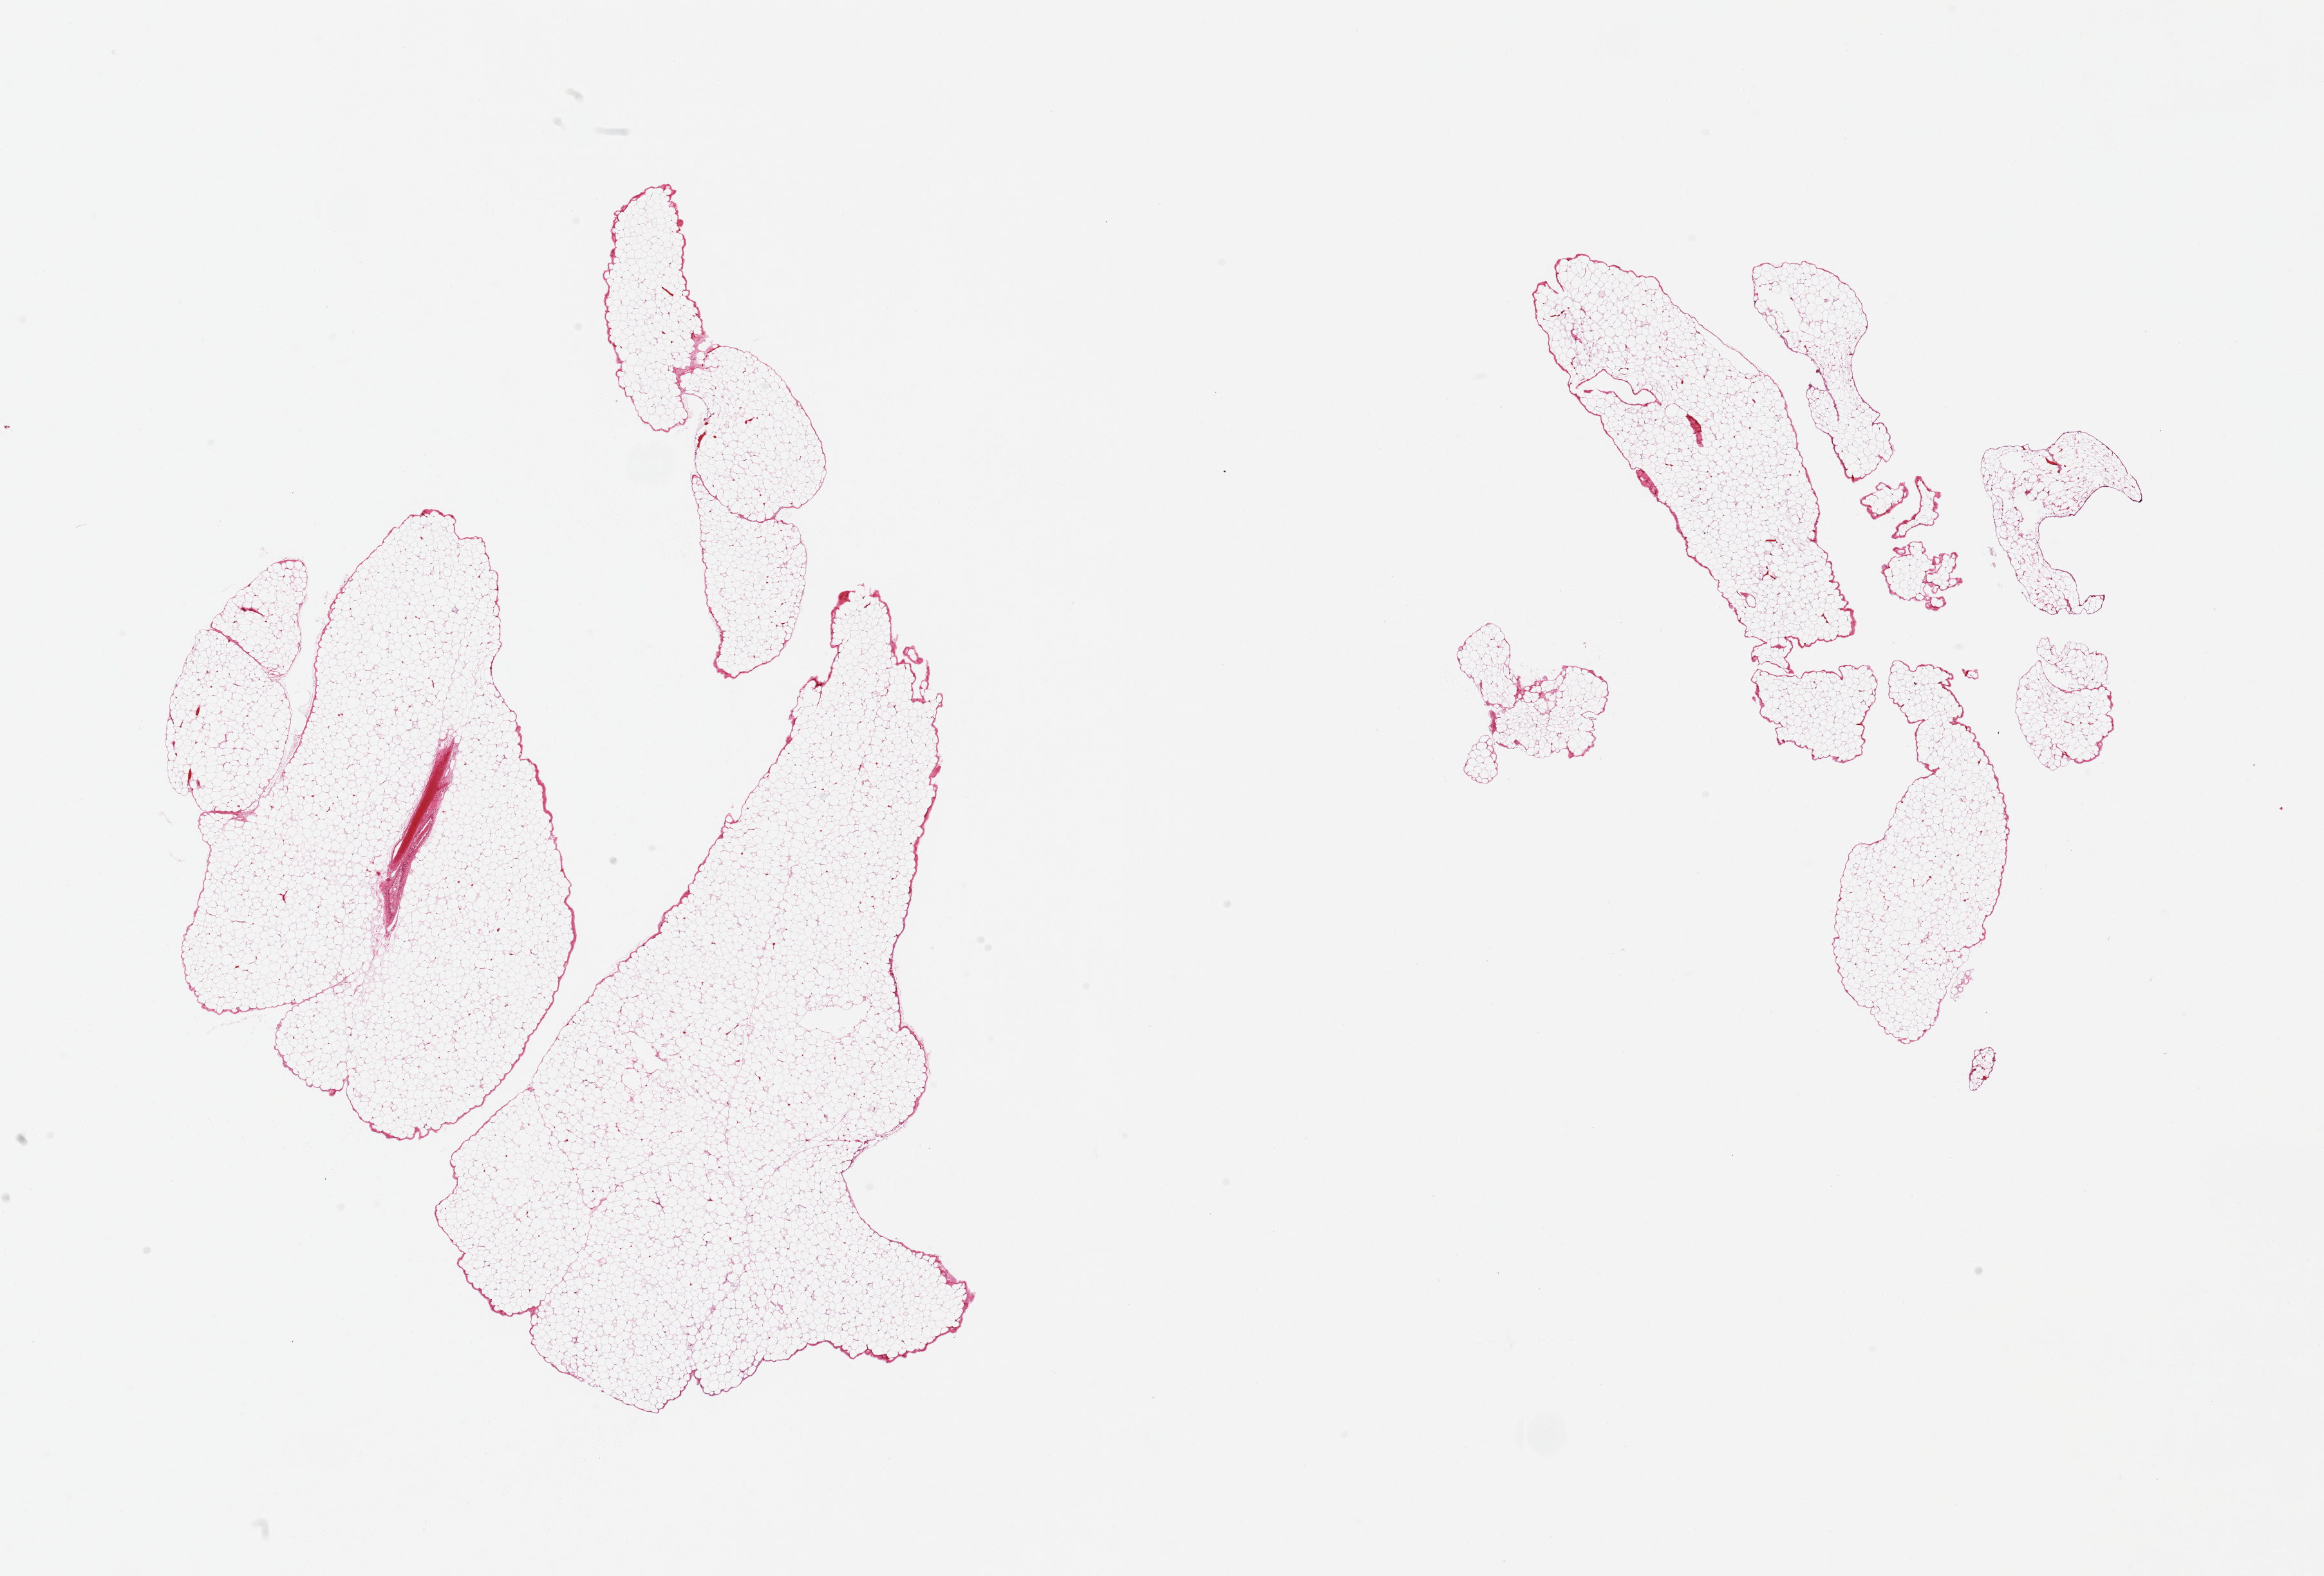
Digitized haematoxylin and eosin-stained section, brightfield — shown as a low-resolution overview of the whole scanned area (about 28.5 x 19.4 mm); PAXgene-fixed paraffin-embedded (PFPE) section; target tissue: omentum; donor tissue sample. Donor: male.
Review note (as recorded): 2 pieces; lobulated mature adipose tissue.